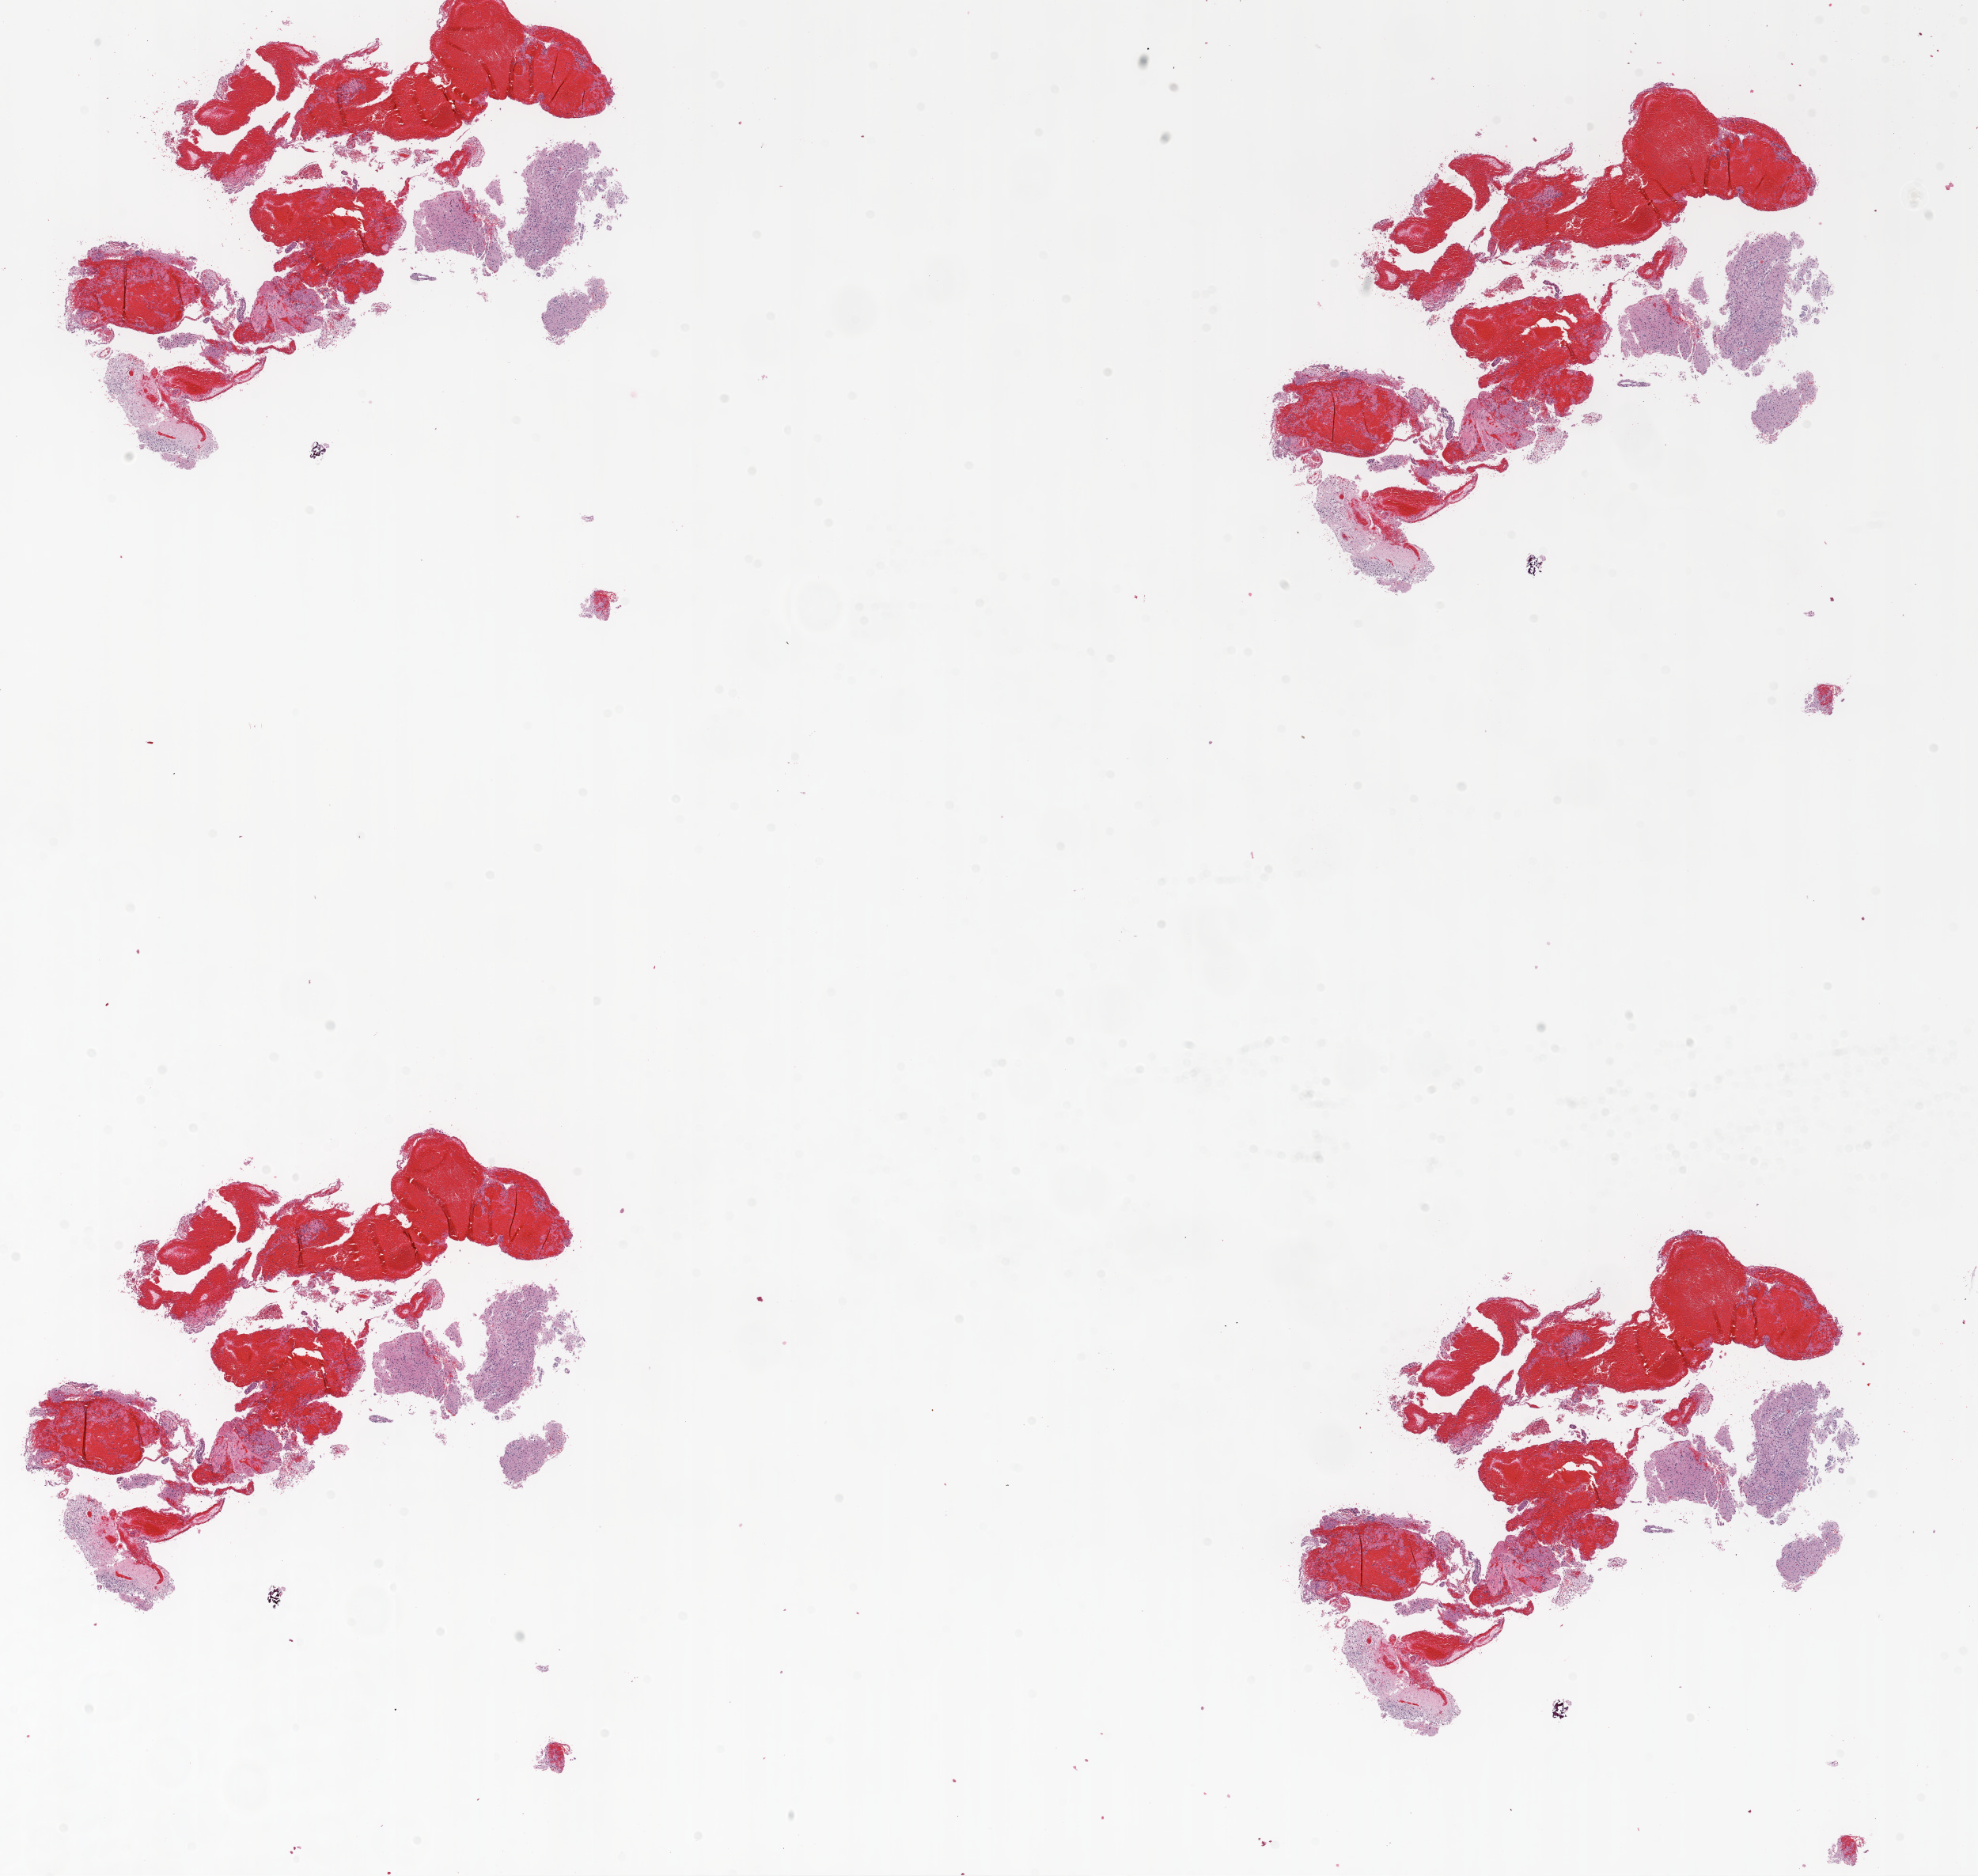
Whole-slide histology image, H&E-stained — a low-resolution overview of the entire scanned area, about 20.1 x 19.0 mm (acquisition: 20x scan), formalin-fixed paraffin-embedded (FFPE) diagnostic section, sample: primary tumour, brain. Patient: male, age at initial diagnosis 30 years.
Histologic diagnosis: Glioblastoma.